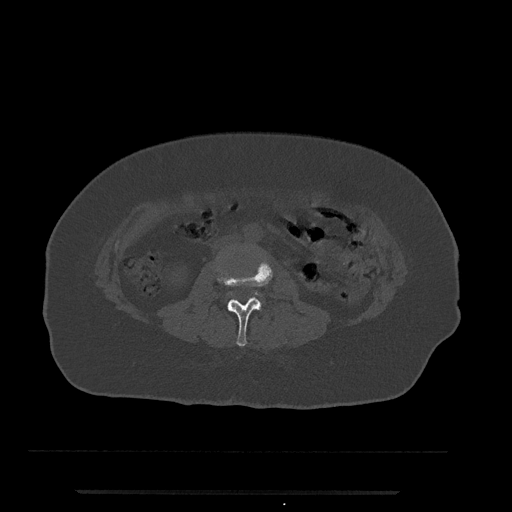
CT including the spine, one axial slice; slice 13 of 797 in the series (ordered by position); reconstruction kernel Br40s/3; bone window (W 1800 / L 400 HU); 512 × 512 image matrix, field of view 440 × 440 mm. Patient: female, 51 years. Case-level facts recorded for this patient, not image findings: primary cancer: neuro.
Outlined on this slice (semi-automatically segmented with operator editing):
- L2 vertebra: bounding box (x1, y1, x2, y2) in pixels: (216, 257, 273, 347)